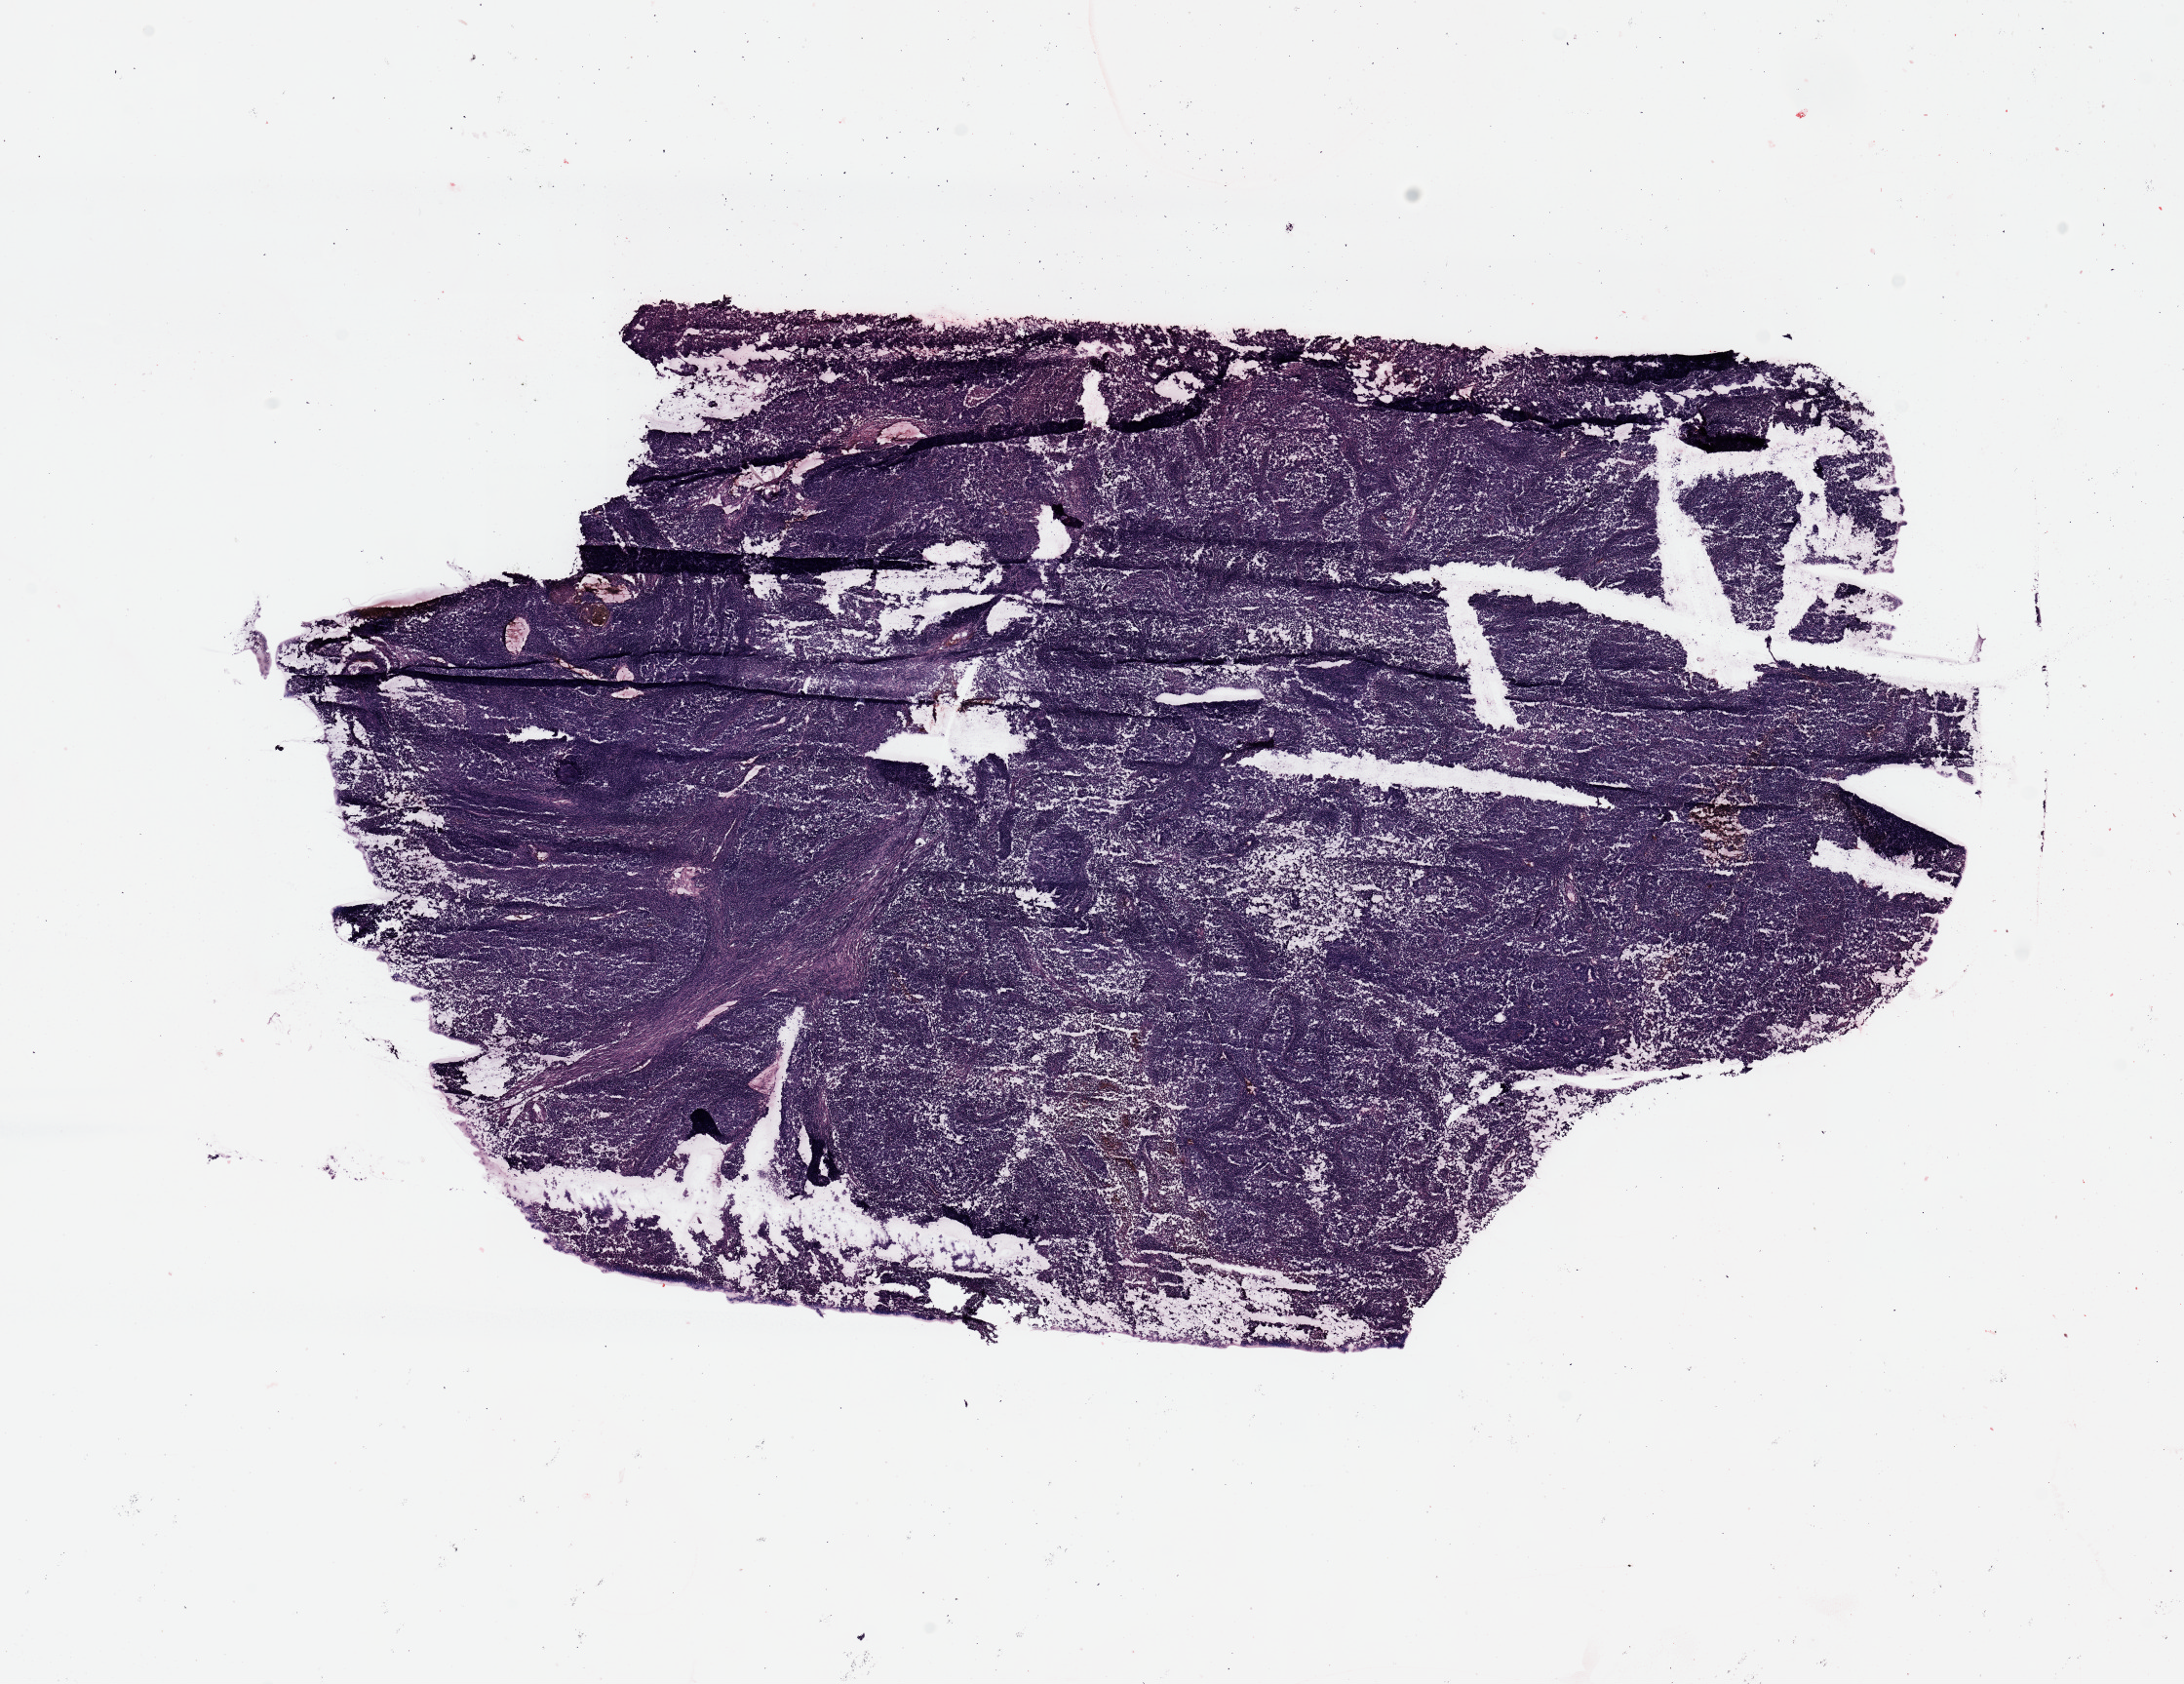
Whole-slide histology image, H&E, whole scanned area (about 17.7 x 13.7 mm, slide scanned at 20x) shown as a low-resolution overview, uterus, tumour tissue. Patient: female, age 62 years. Histologic grade: G3 (poorly differentiated).
• AJCC pathologic stage: I
• diagnosis: Endometrioid adenocarcinoma, NOS